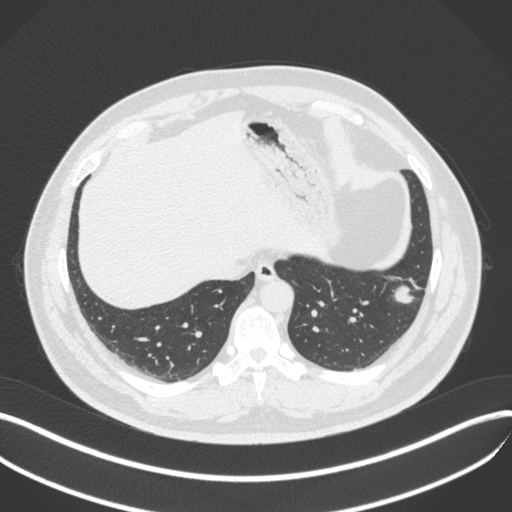
Chest CT, one axial slice; reconstruction kernel B31f; lung window (W 1500 / L -600 HU); 512 × 512 image matrix. Male patient, age 39 years. From the clinical record (not read from this slice): clinical TNM (as recorded): T2a N0 M0; histopathological grade: G2-3.
Structures marked on this image (bounding box drawn by a radiologist):
- lung tumour (recorded histology: adenocarcinoma): bounding box [x1, y1, x2, y2] px = [391, 278, 417, 308]